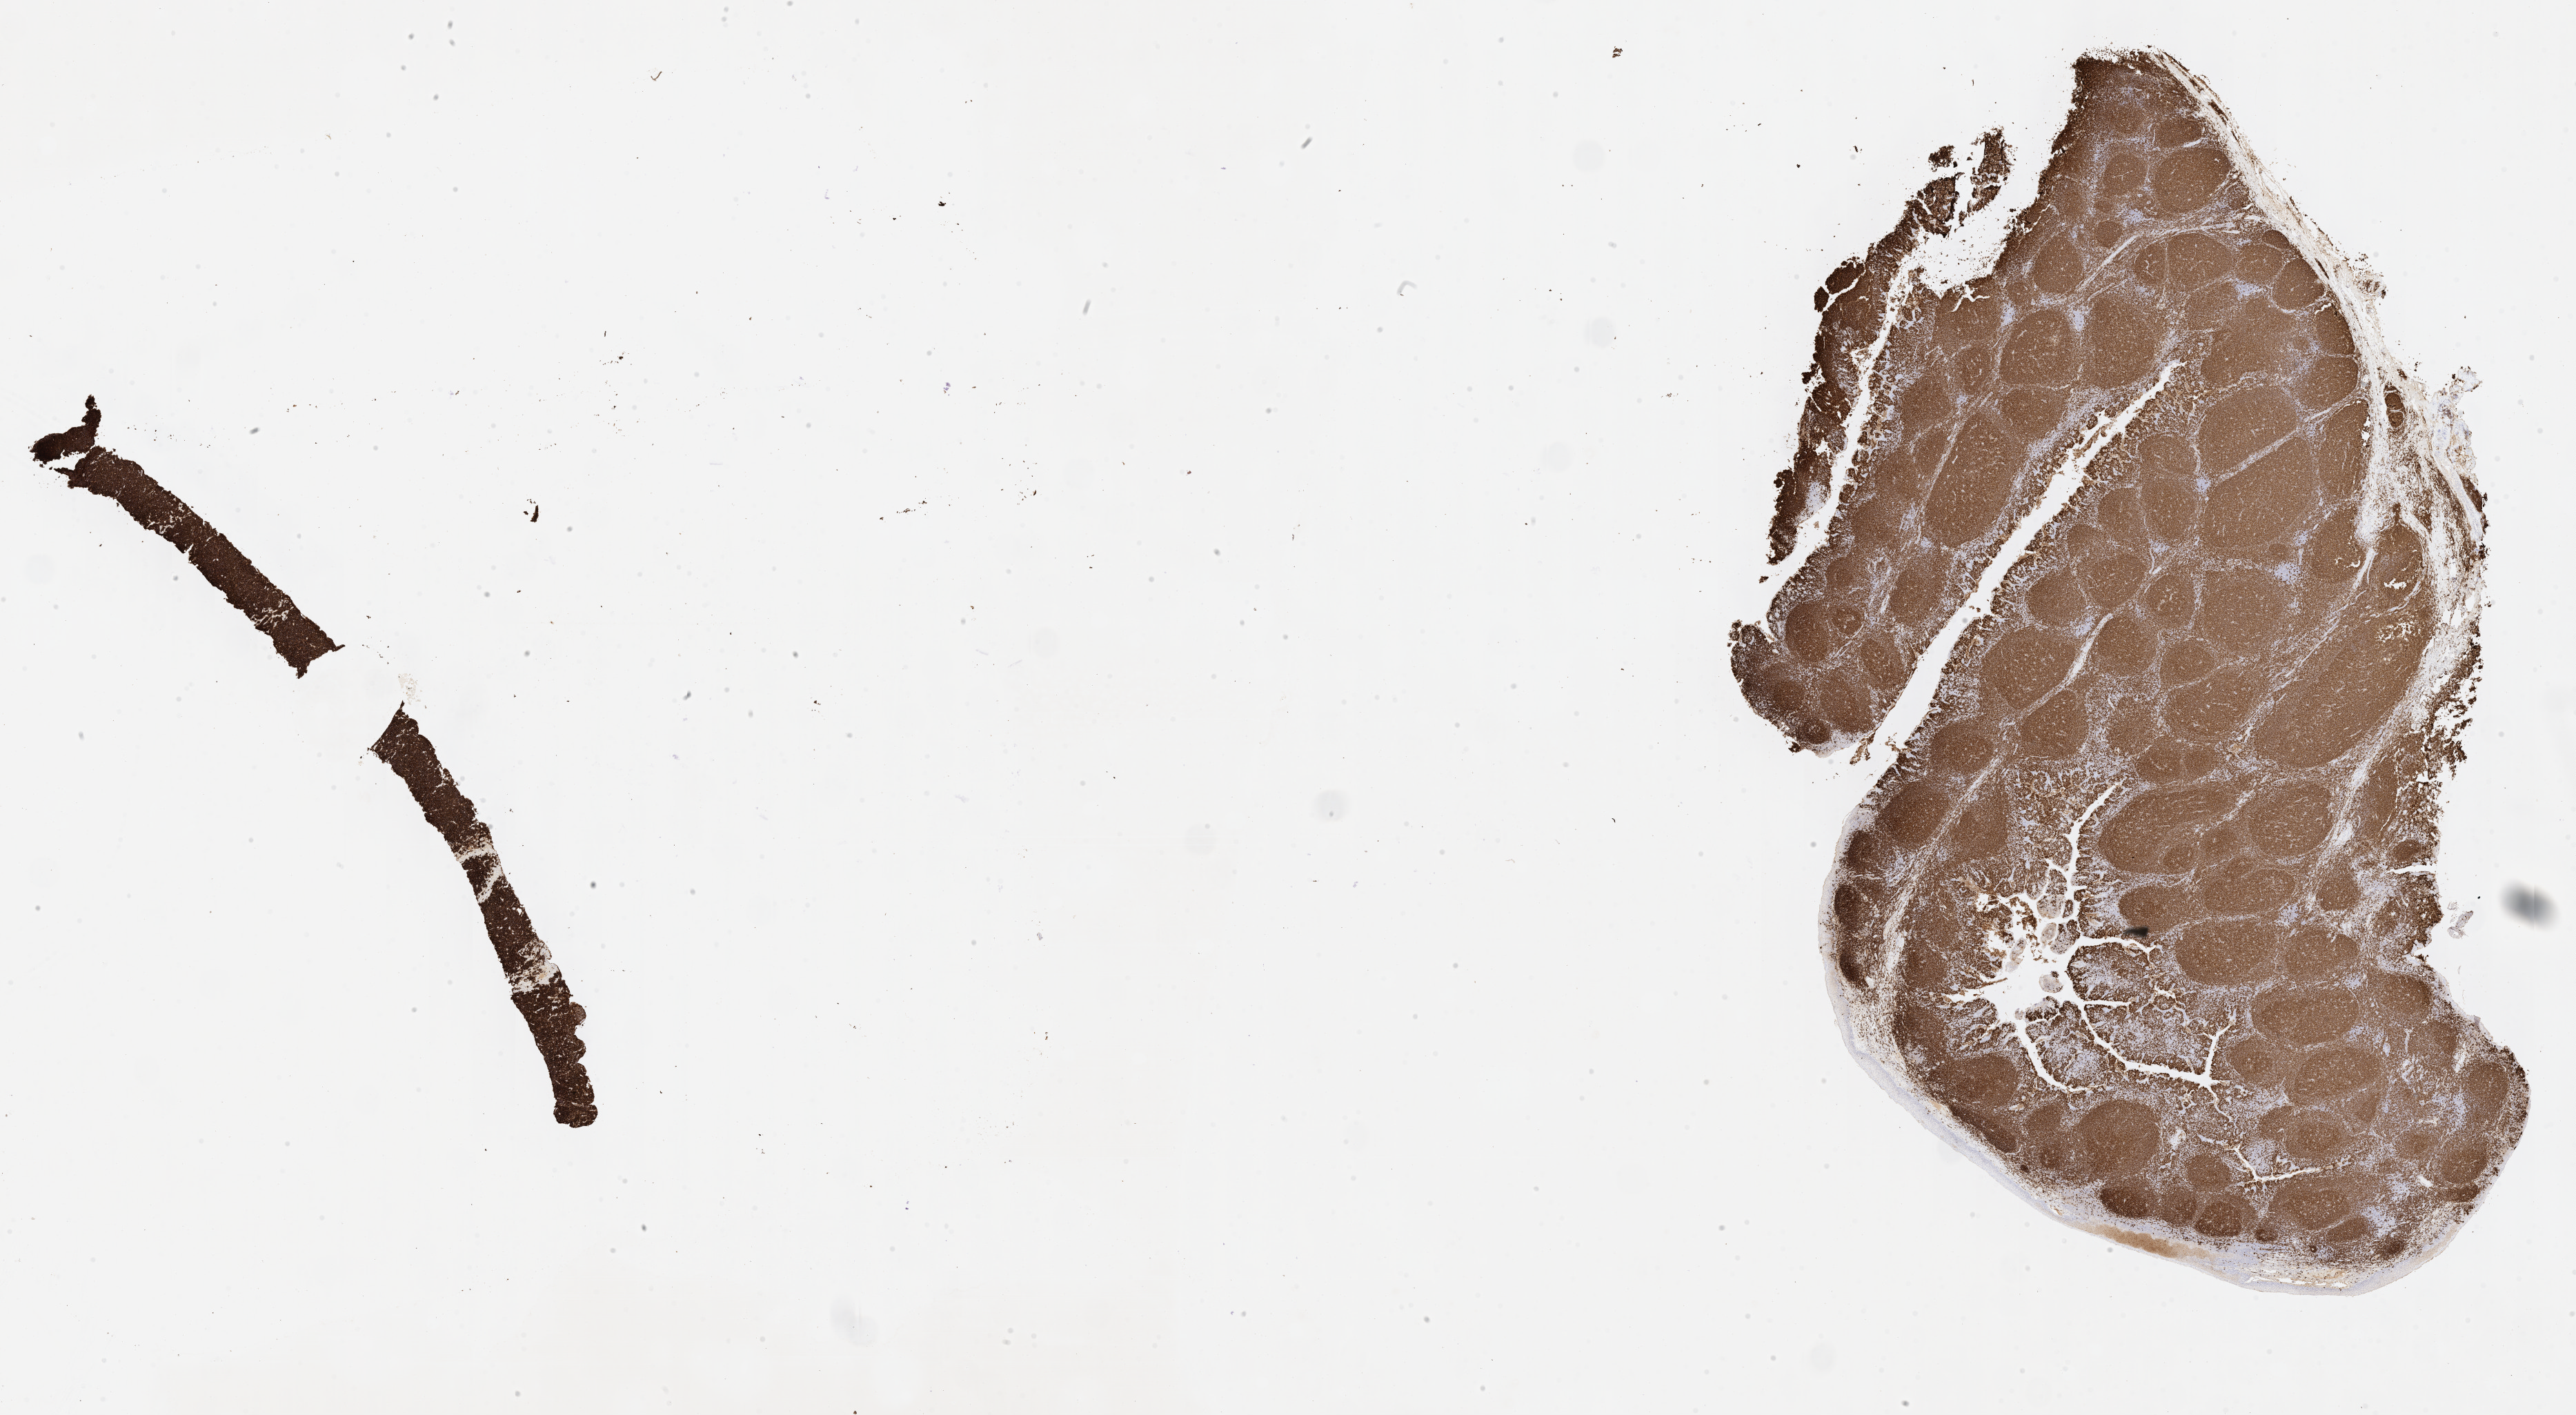
Whole-slide image, immunohistochemical stain for CD20, shown as a low-resolution overview of the whole scanned area (about 30.2 x 16.6 mm). Female patient.
* specimen: tumor tissue